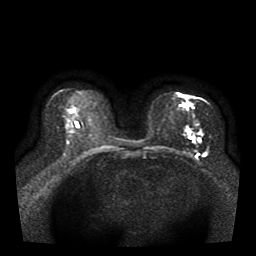
Breast MRI, one axial slice; position 21 of 41 along the scan axis; diffusion-weighted series; image 2 of 4 stored at this slice position (different b-values; order by instance number); 1.5 T; 5 mm slice thickness; 256 × 256 image matrix, field of view 330 × 330 mm. Female patient.
Annotated regions visible in this slice (expert manual segmentation):
- tumour on diffusion-weighted imaging: bounding box [x1, y1, x2, y2] px = [180, 105, 208, 157]